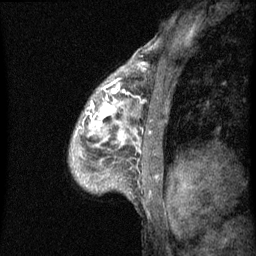
Breast MRI (dynamic contrast-enhanced), one sagittal slice; position 42 of 60 along the scan axis; dynamic contrast-enhanced series, image 2 of 3 at this slice position (ordered by acquisition); 1.5 T; TE 4.2 ms, TR 8 ms; 2 mm slice thickness; 256 × 256 image matrix. Patient: female, 50 years.
Annotated regions visible in this slice (semi-automatic segmentation, software-assisted and operator-edited):
- analysis volume of interest (the breast-tissue region the enhancement analysis was run in; not a lesion): bounding box <68,64,141,187> (left, top, right, bottom; pixels)
- tumour enhancement mask (voxels above the 70 % enhancement threshold inside the analysis volume of interest): <83,64,140,145>